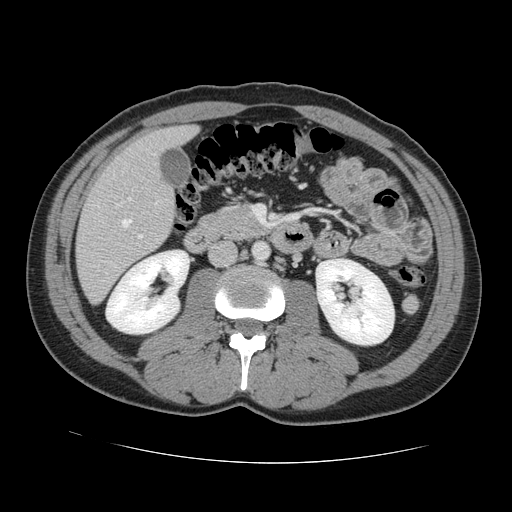
Contrast-enhanced abdominal CT, one axial slice; slice 48 of 131 in the series (ordered by position); intravenous contrast given; soft-tissue window (W 400 / L 40 HU); 2.5 mm slice thickness; 512 × 512 image matrix. Male patient, age 40 years. From the clinical record (not read from this slice): diagnosis: colorectal cancer liver metastases, imaged before liver resection; multiple liver metastases: yes.
Outlined on this slice (expert manual segmentation):
- hepatic veins: bounding box (x1, y1, x2, y2) in pixels: (122, 219, 131, 227)
- liver: (77, 127, 195, 303)
- planned liver remnant (the part of the liver to remain after resection): (123, 126, 196, 167)
- portal vein (with intrahepatic branches): (128, 198, 143, 239)